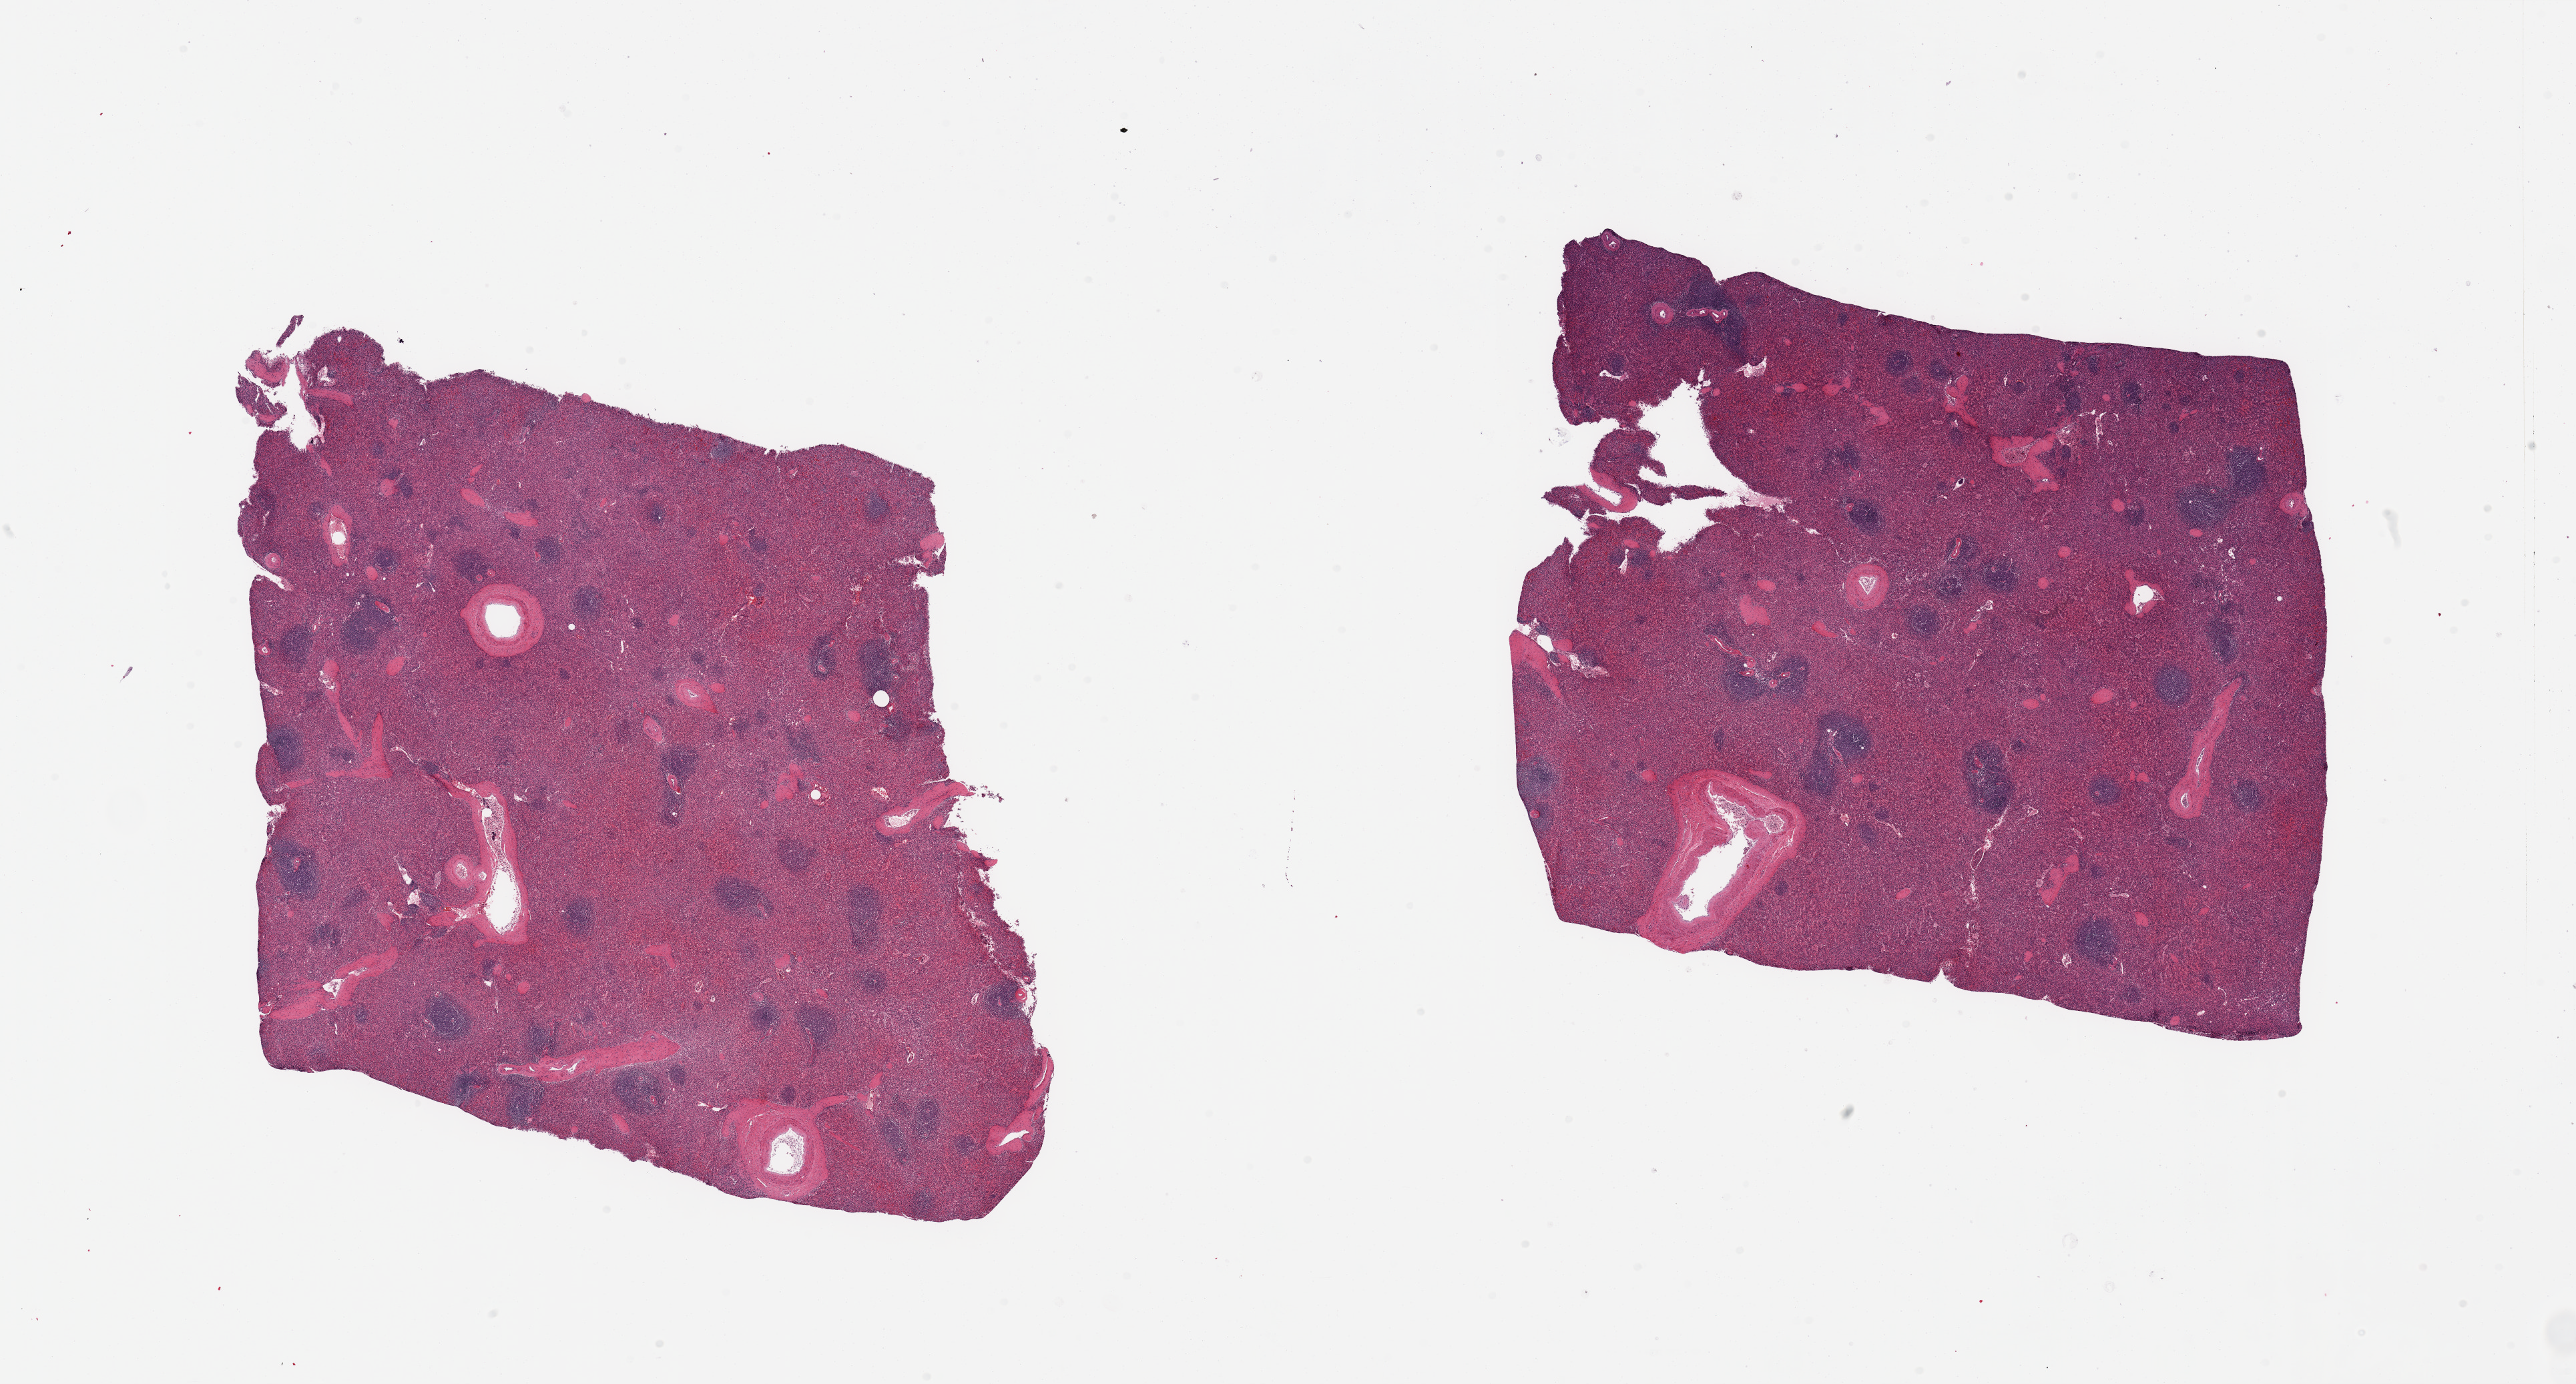
Haematoxylin and eosin whole-slide image — a low-resolution overview of the entire scanned area, about 30.5 x 16.4 mm (acquisition: 20x scan). PAXgene-fixed, paraffin-embedded tissue. Section of spleen (target tissue). Donor tissue sample. Donor: male.
• review note (as recorded): 2 pieces, no abnormalities